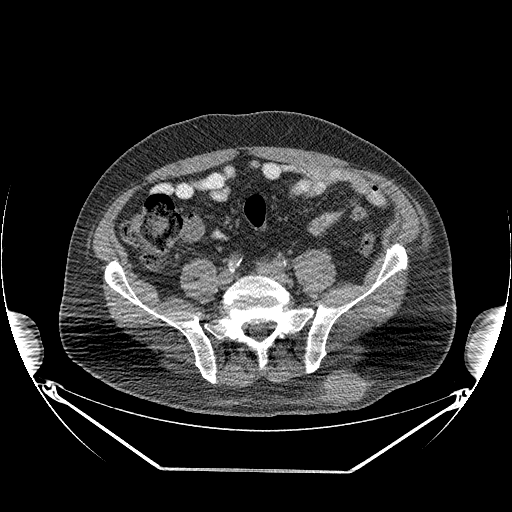
CT of an extremity soft-tissue mass (from a PET/CT study), one axial slice. Position 93 of 267 along the scan axis. Reconstruction kernel STANDARD. 140 kVp. Soft-tissue window (W 400 / L 40 HU). 3.75 mm slice thickness. 512 × 512 image matrix, field of view 500 × 500 mm. Male patient. Case-level facts recorded for this patient, not image findings: histological type: pleiomorphic leiomyosarcoma; grade: high; site of the primary tumour: left buttock.
Annotated regions visible in this slice (expert contour drawn on MRI and transferred to this co-registered scan by the dataset authors):
- gross tumour volume including surrounding oedema: bounding box [x1, y1, x2, y2] px = [320, 372, 362, 407]
- gross tumour volume (mass): [322, 372, 362, 407]